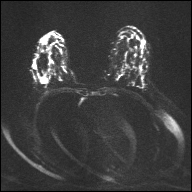
Breast MRI, one axial slice. Slice 21 of 32 in the series (ordered by position). Diffusion-weighted series; image 2 of 4 stored at this slice position (different b-values; order by instance number). 1.5 T. 4 mm slice thickness. 192 × 192 image matrix, field of view 360 × 360 mm. Female patient.
Structures marked on this image (outlined manually by an expert reader):
- tumour on diffusion-weighted imaging: bounding box <33,64,47,83> (left, top, right, bottom; pixels)